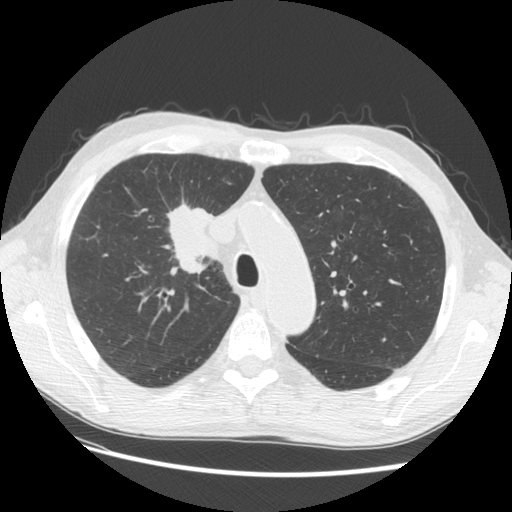
Chest CT (low-dose screening protocol), one axial image. Third screening round (two years after baseline). Lung window (W 1500 / L -600 HU). 2.5 mm slice thickness. Male, age 73 years at enrolment. Current smoker at enrolment.
Expert-annotated lung lesion, bounding box (x1, y1, x2, y2) in pixels: (142, 183, 233, 278). The screening reader recorded 4 non-calcified nodules or masses ≥4 mm on this exam (right upper lobe, right upper lobe, right upper lobe, left lower lobe); which of them this box marks is not recorded. Official screen result: positive, other. Later outcome: lung cancer diagnosed 48 days after this screen — squamous cell carcinoma, NOS, right upper lobe, poorly differentiated (G3), stage IIIB (AJCC 6th edition), 56 mm at pathology.